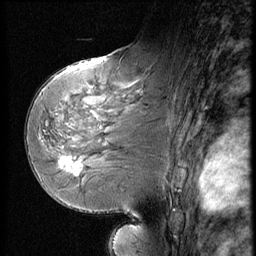
Breast MRI (dynamic contrast-enhanced), one sagittal slice; slice 31 of 56 in the series (ordered by position); dynamic contrast-enhanced series, image 2 of 3 at this slice position (ordered by acquisition); 1.5 T; TE 4.2 ms, TR 9 ms; 2.5 mm slice thickness; 256 × 256 image matrix, field of view 180 × 180 mm. Female patient, age 58 years. Case-level facts recorded for this patient, not image findings: setting: breast cancer imaged before/during neoadjuvant chemotherapy; receptor status: HR-positive, HER2-negative.
Structures marked on this image (semi-automatic segmentation, software-assisted and operator-edited):
- analysis volume of interest (the breast-tissue region the enhancement analysis was run in; not a lesion): bounding box (x1, y1, x2, y2) in pixels: (51, 147, 96, 185)
- tumour enhancement mask (voxels above the 140 % enhancement threshold inside the analysis volume of interest): (59, 158, 81, 175)